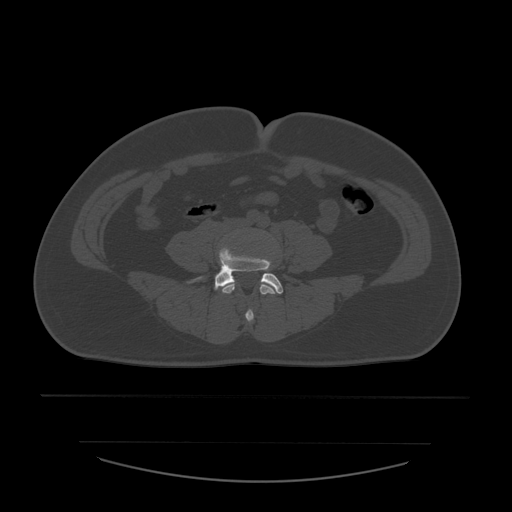
CT including the spine, one axial slice; position 131 of 532 along the scan axis; reconstruction kernel STANDARD; 120 kVp; bone window (W 1800 / L 400 HU); 1.25 mm slice thickness; 512 × 512 image matrix. Patient age 44 years. From the clinical record (not read from this slice): primary cancer: soft tissue sarcoma.
Structures marked on this image (semi-automatically segmented with operator editing):
- L4 vertebra: box from (x=222, y=283) to (x=278, y=323) px
- L5 vertebra: (x=214, y=249)–(x=283, y=294)